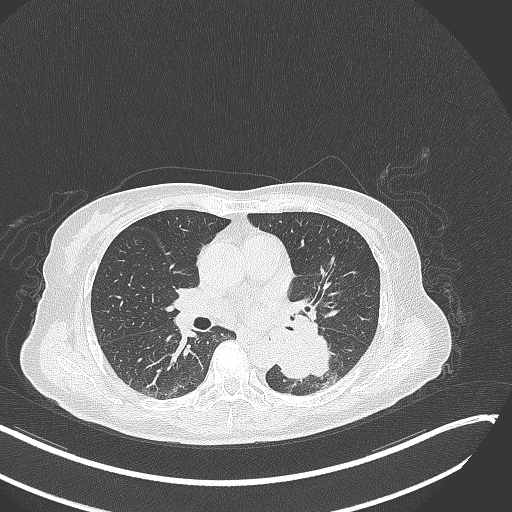
Chest CT, one axial slice. Slice 146 of 342 in the series (ordered by position). Reconstruction kernel B70f. Lung window (W 1500 / L -600 HU). 1 mm slice thickness. 512 × 512 image matrix, field of view 400 × 400 mm. Patient: female, 64 years. From the clinical record (not read from this slice): clinical TNM (as recorded): T3 N1 M1; histopathological grade: G3.
Structures marked on this image (bounding box drawn by a radiologist):
- lung tumour (recorded histology: small cell carcinoma): bounding box <269,324,336,384> (left, top, right, bottom; pixels)